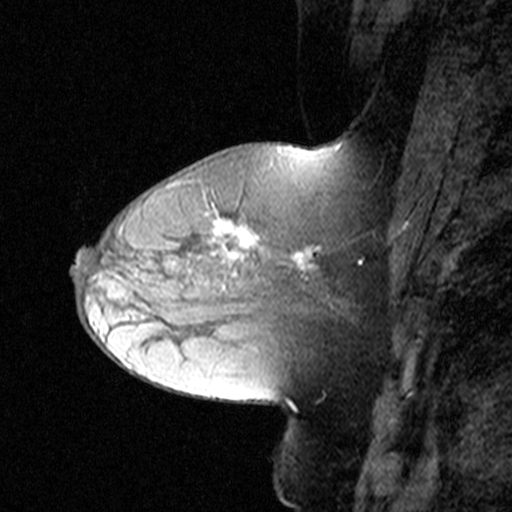
Breast MRI (dynamic contrast-enhanced), one sagittal slice. Slice 18 of 44 in the series (ordered by position). Dynamic contrast-enhanced study with each time point stored as its own series, time point 2 of 3 at this slice position (early post-contrast, ordered by acquisition time). 1.5 T. TE 4.5 ms, TR 11 ms. 3 mm slice thickness. 512 × 512 image matrix, field of view 200 × 200 mm. Patient: female, 50 years. From the clinical record (not read from this slice): setting: breast cancer imaged before/during neoadjuvant chemotherapy; receptor status: HR-positive, HER2-negative.
Outlined on this slice (semi-automatically segmented with operator editing):
- analysis volume of interest (the breast-tissue region the enhancement analysis was run in; not a lesion): bounding box <180,198,330,311> (left, top, right, bottom; pixels)
- tumour enhancement mask (voxels above the 90 % enhancement threshold inside the analysis volume of interest): <212,220,322,291>